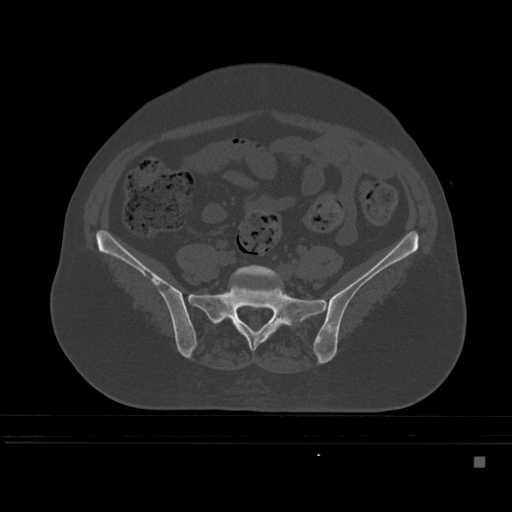
CT including the spine, one axial slice; position 97 of 495 along the scan axis; bone window (W 1800 / L 400 HU); 1.5 mm slice thickness; 512 × 512 image matrix, field of view 404 × 404 mm. Patient: female, 33 years. Case-level facts recorded for this patient, not image findings: primary cancer: breast.
Structures marked on this image (semi-automatically segmented with operator editing):
- L5 vertebra: box from (x=226, y=265) to (x=288, y=317) px